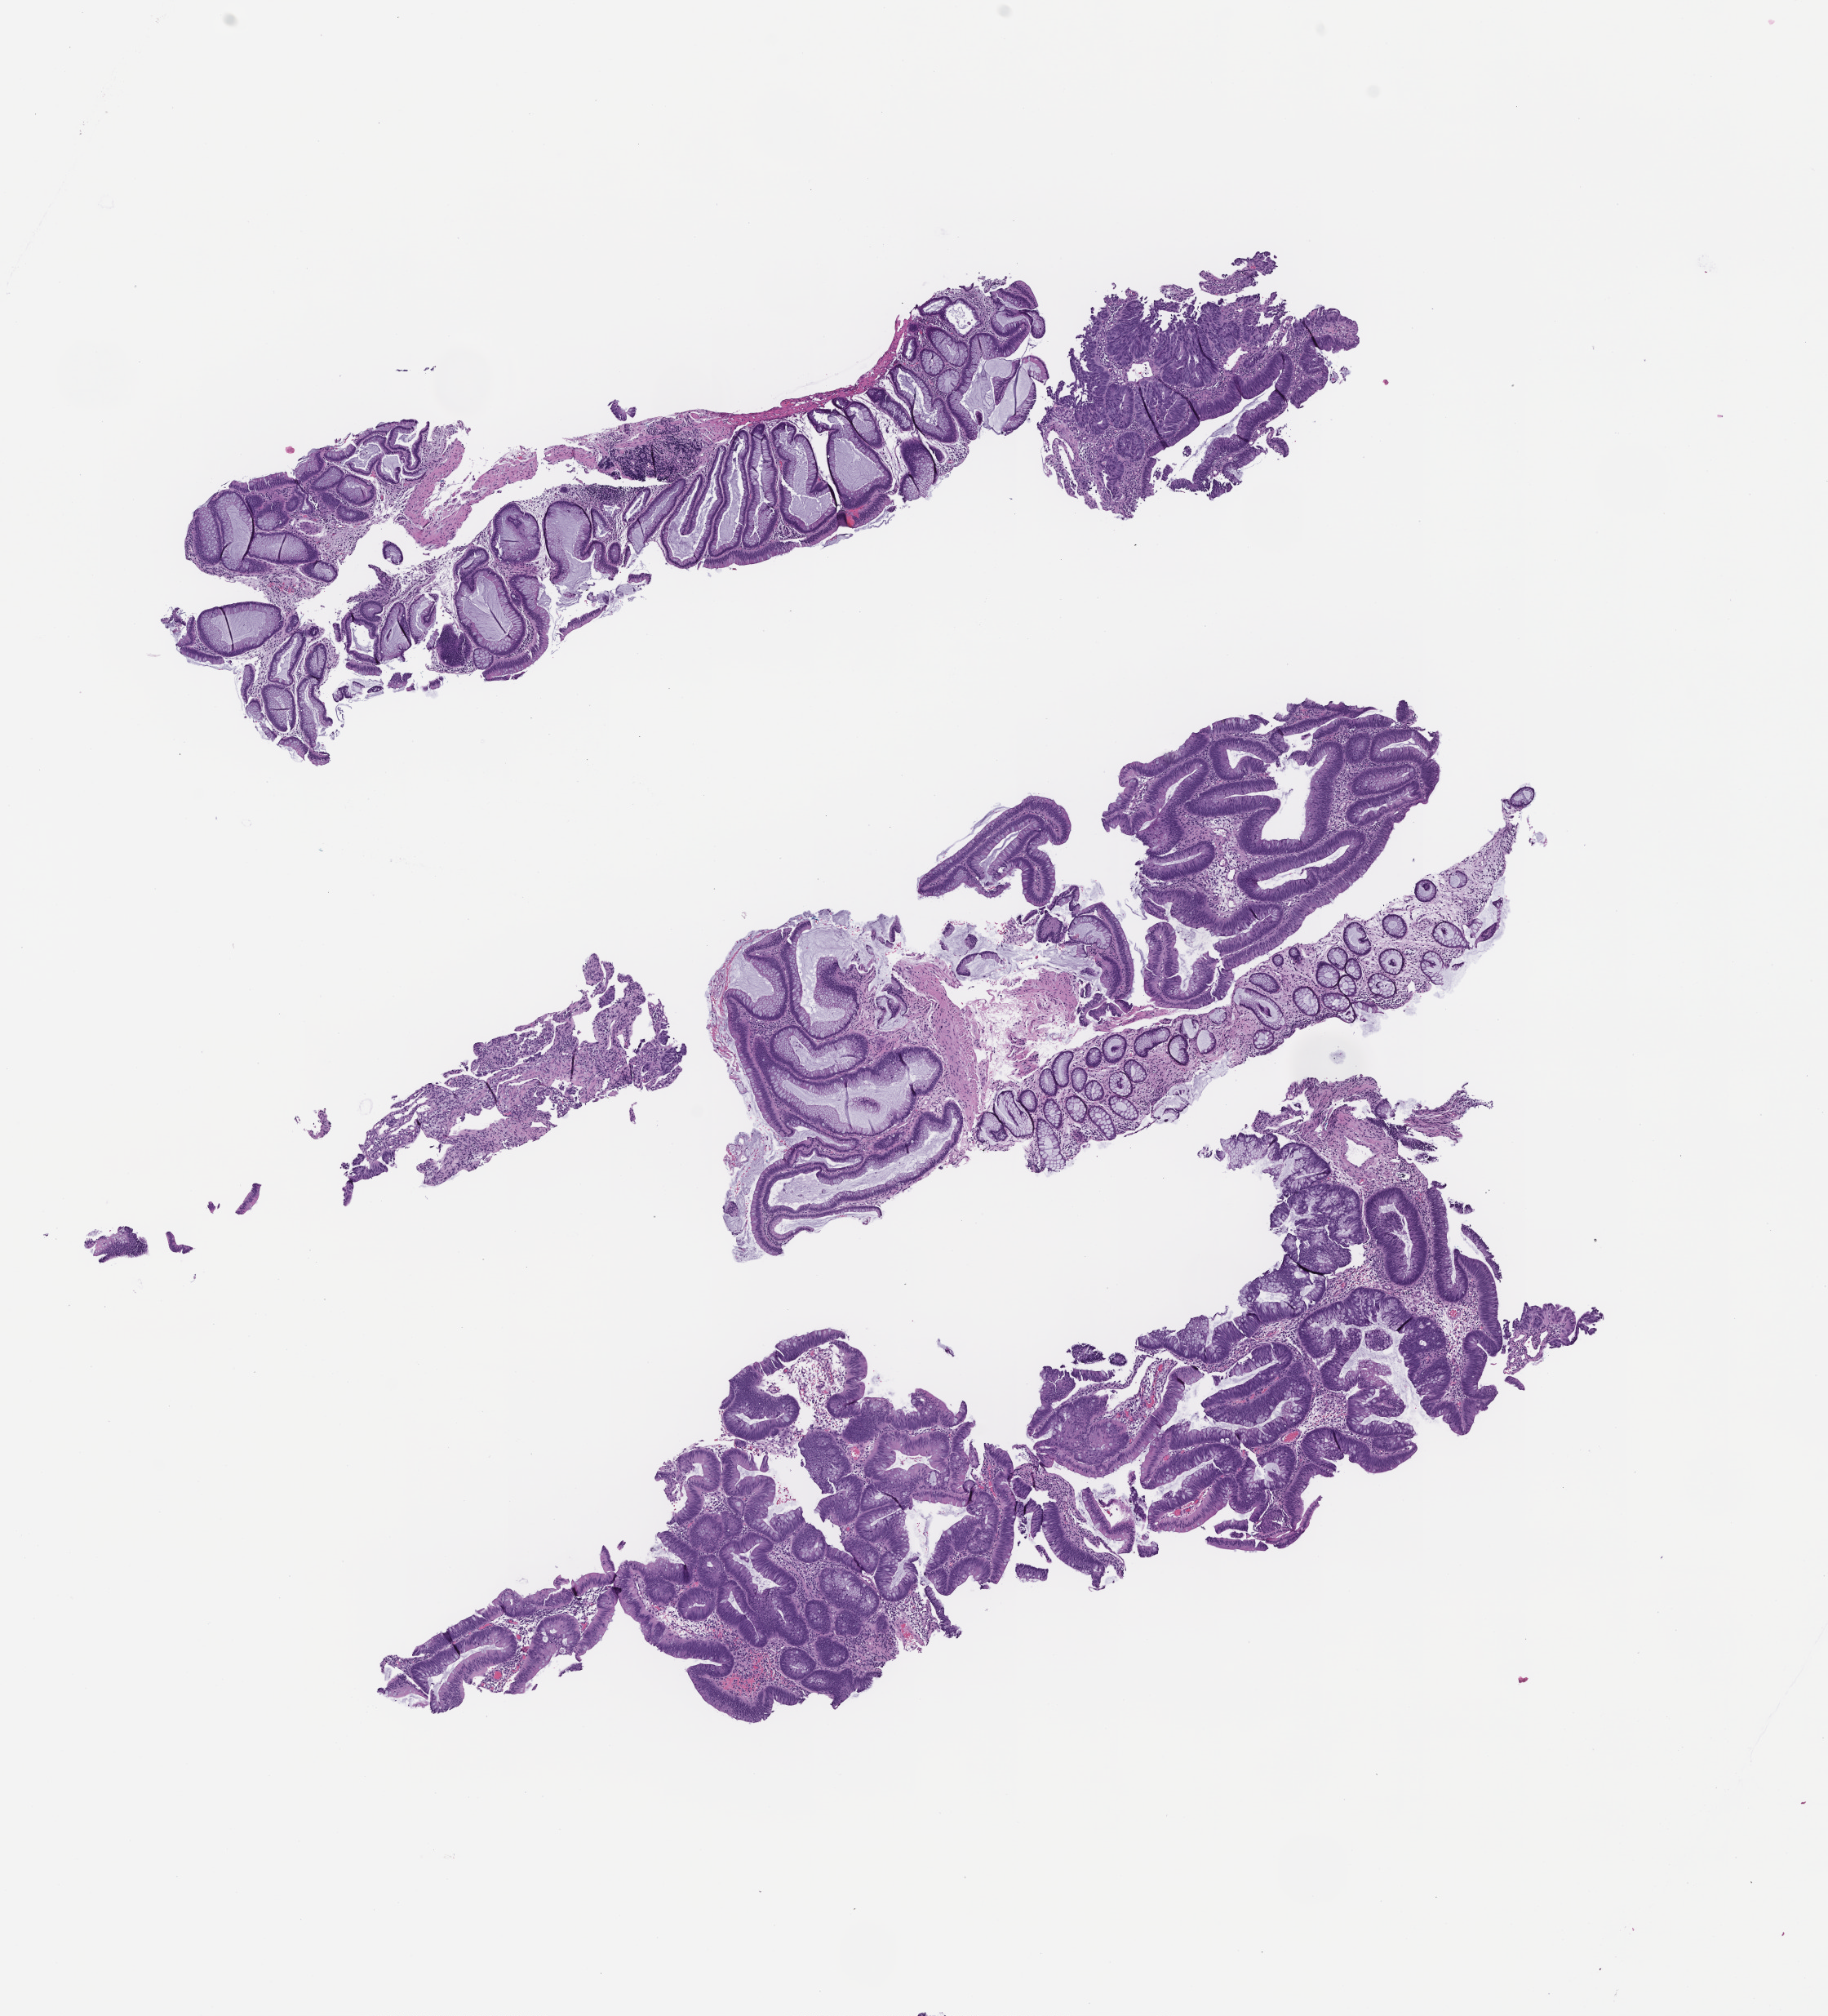
Hematoxylin and eosin (H&E) whole-slide image, a low-resolution overview of the entire scanned area, about 9.0 x 10.0 mm, formalin-fixed paraffin-embedded section, site: rectum. Patient: female.
This section: primary tumour tissue. Diagnosis: Colorectal Carcinoma.